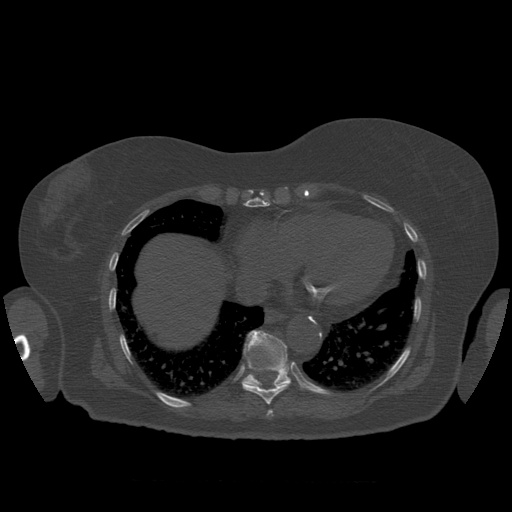
CT including the spine, one axial slice; position 352 of 399 along the scan axis; reconstruction kernel STANDARD; bone window (W 1800 / L 400 HU); 1.25 mm slice thickness; 512 × 512 image matrix, field of view 404 × 404 mm. Patient age 81 years. Case-level facts recorded for this patient, not image findings: primary cancer: renal.
Annotated regions visible in this slice (semi-automatic segmentation, software-assisted and operator-edited):
- T10 vertebra: bounding box [x1, y1, x2, y2] px = [244, 331, 292, 388]
- T8 vertebra: [267, 410, 273, 416]
- T9 vertebra: [242, 334, 288, 405]